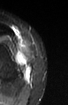
MRI of an extremity soft-tissue mass, one axial slice; position 22 of 52 along the scan axis; STIR; MR volume resampled by the dataset authors to the PET/CT grid (not the native acquisition matrix); 3.27 mm slice thickness; 68 × 105 image matrix, field of view 66 × 103 mm. Female patient. Case-level facts recorded for this patient, not image findings: histological type: spindle cell suggestive of biphasic synovial sarcoma; grade: intermediate; site of the primary tumour: left knee.
Outlined on this slice (expert contour drawn on MRI and transferred to this co-registered scan by the dataset authors):
- gross tumour volume including surrounding oedema: bounding box <15,50,31,81> (left, top, right, bottom; pixels)
- gross tumour volume (mass): <15,52,31,81>